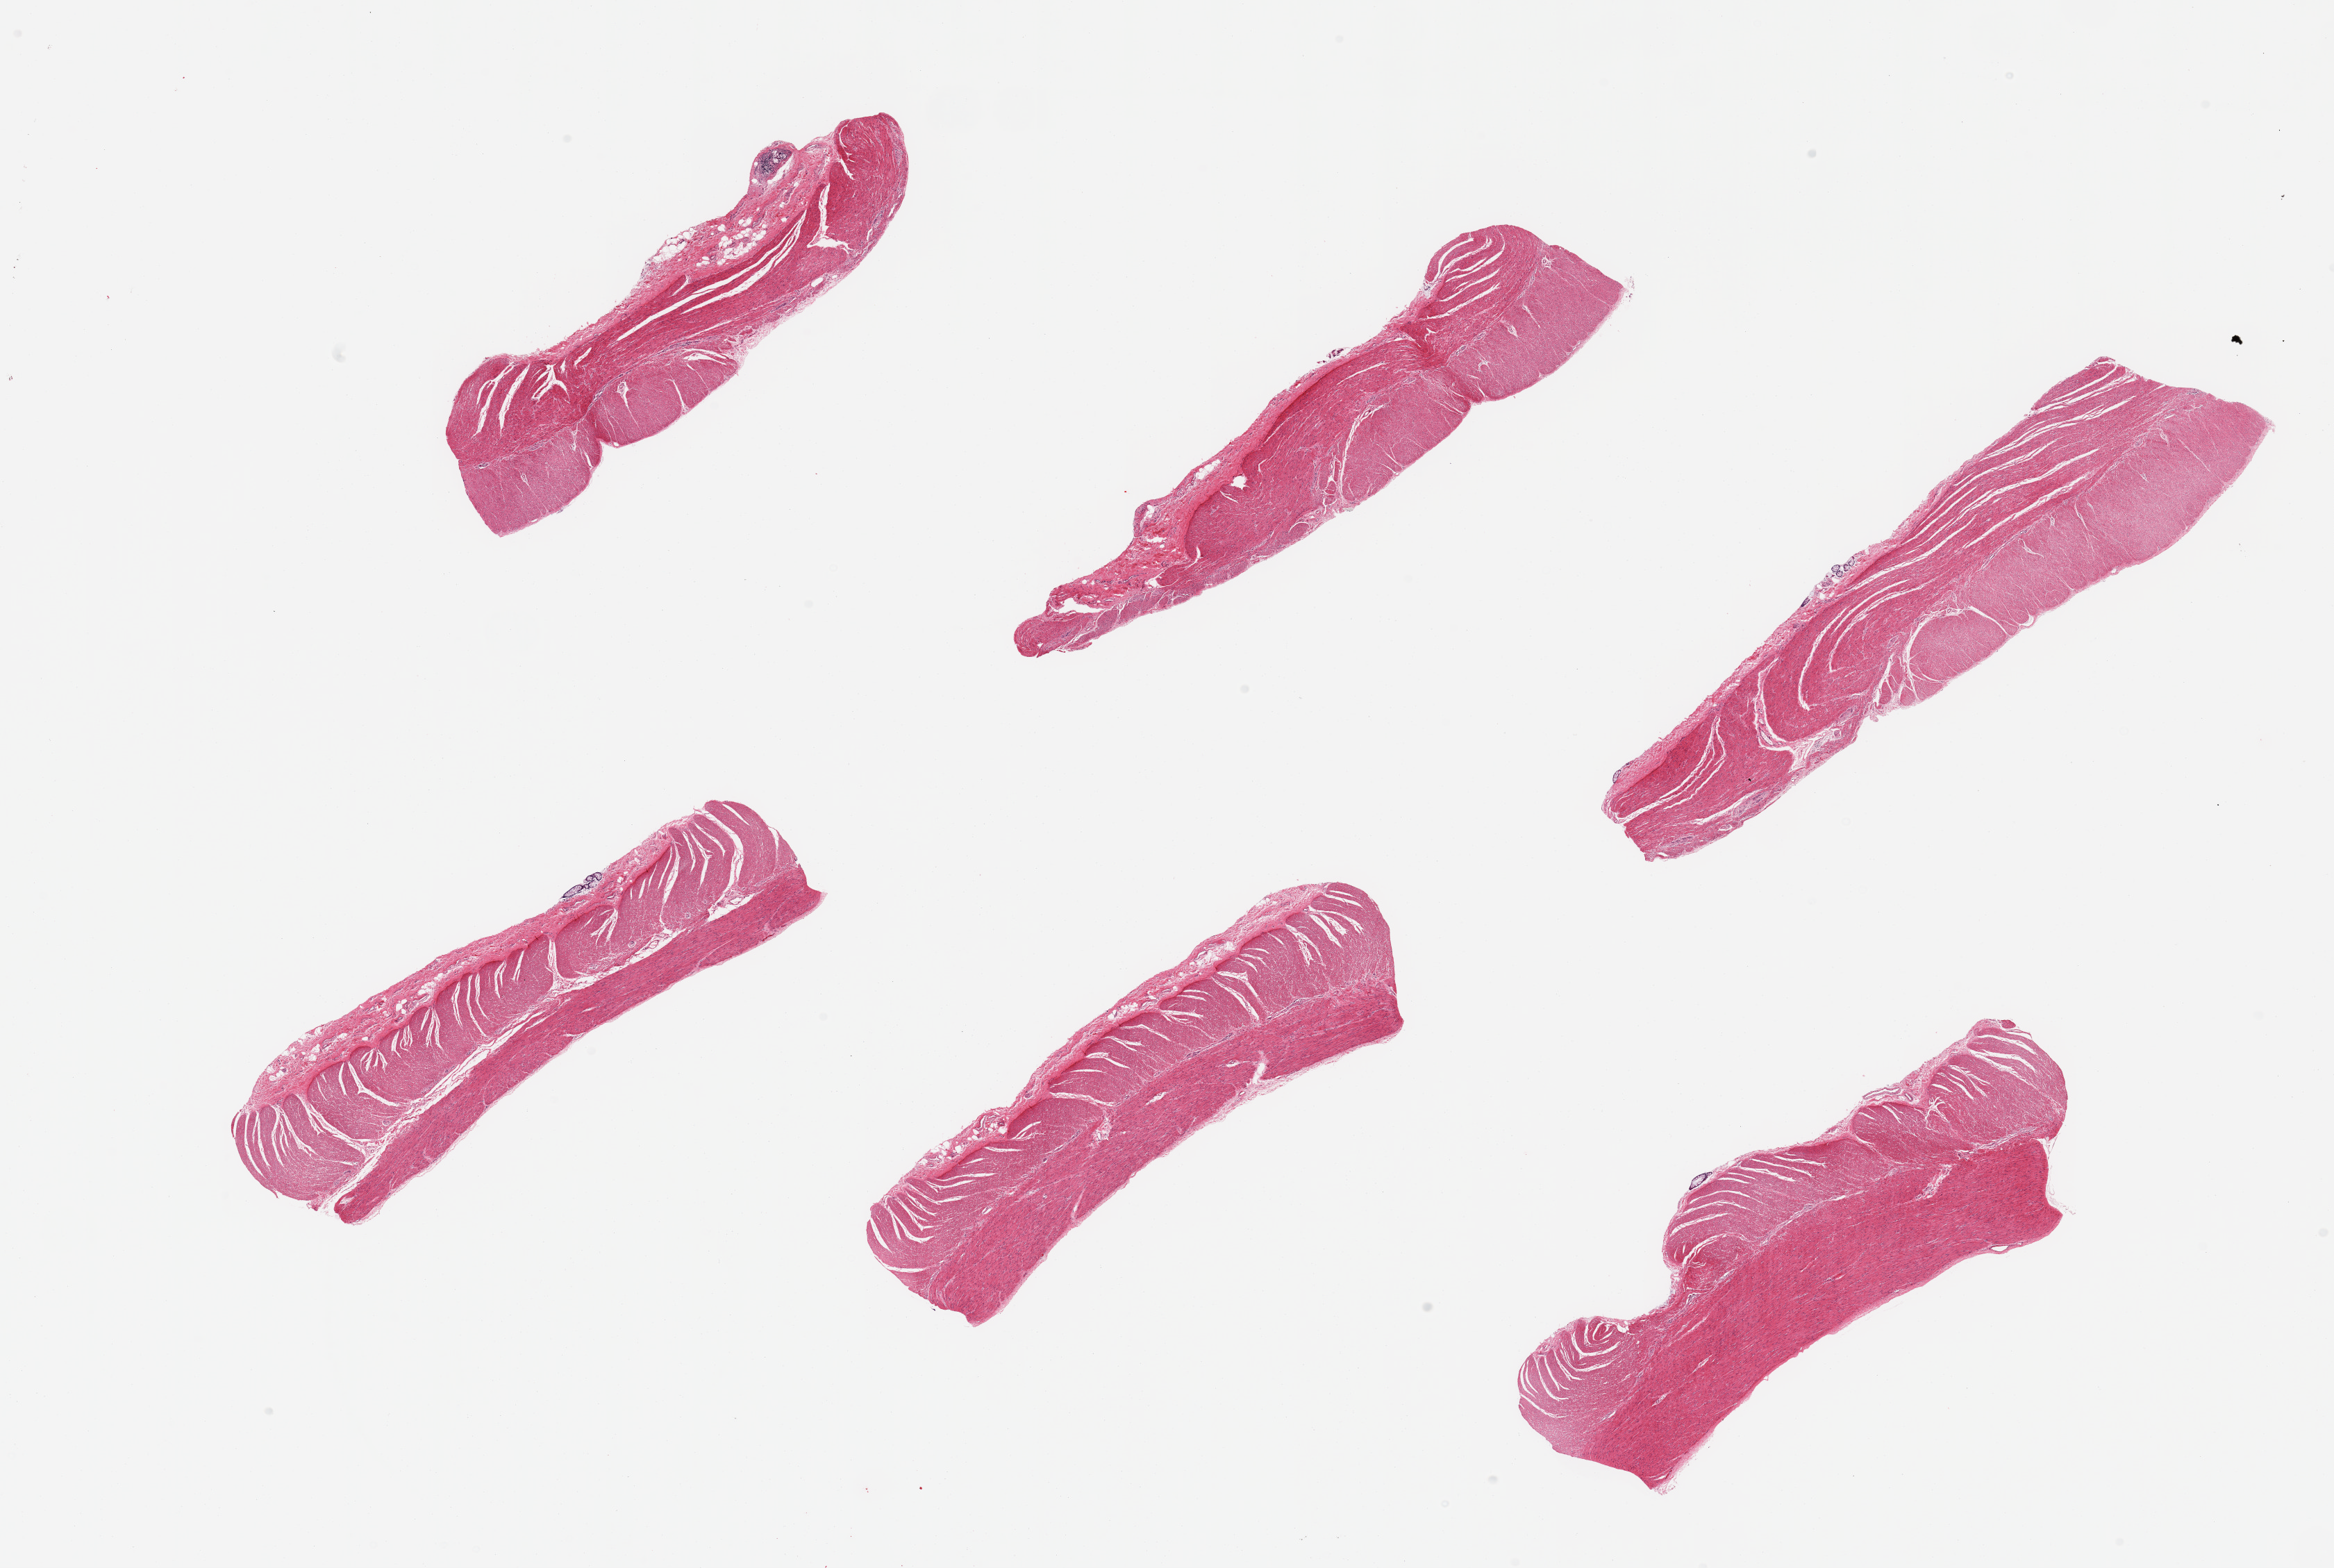
Digitized H&E-stained section — low-resolution overview of the scanned area, about 26.6 x 17.9 mm (from a 20x scan), PAXgene-fixed, paraffin-embedded tissue, section of sigmoid colon (target tissue), tissue donor sample.
Pathologist's review note for this sample: 6 pieces; well dissected.